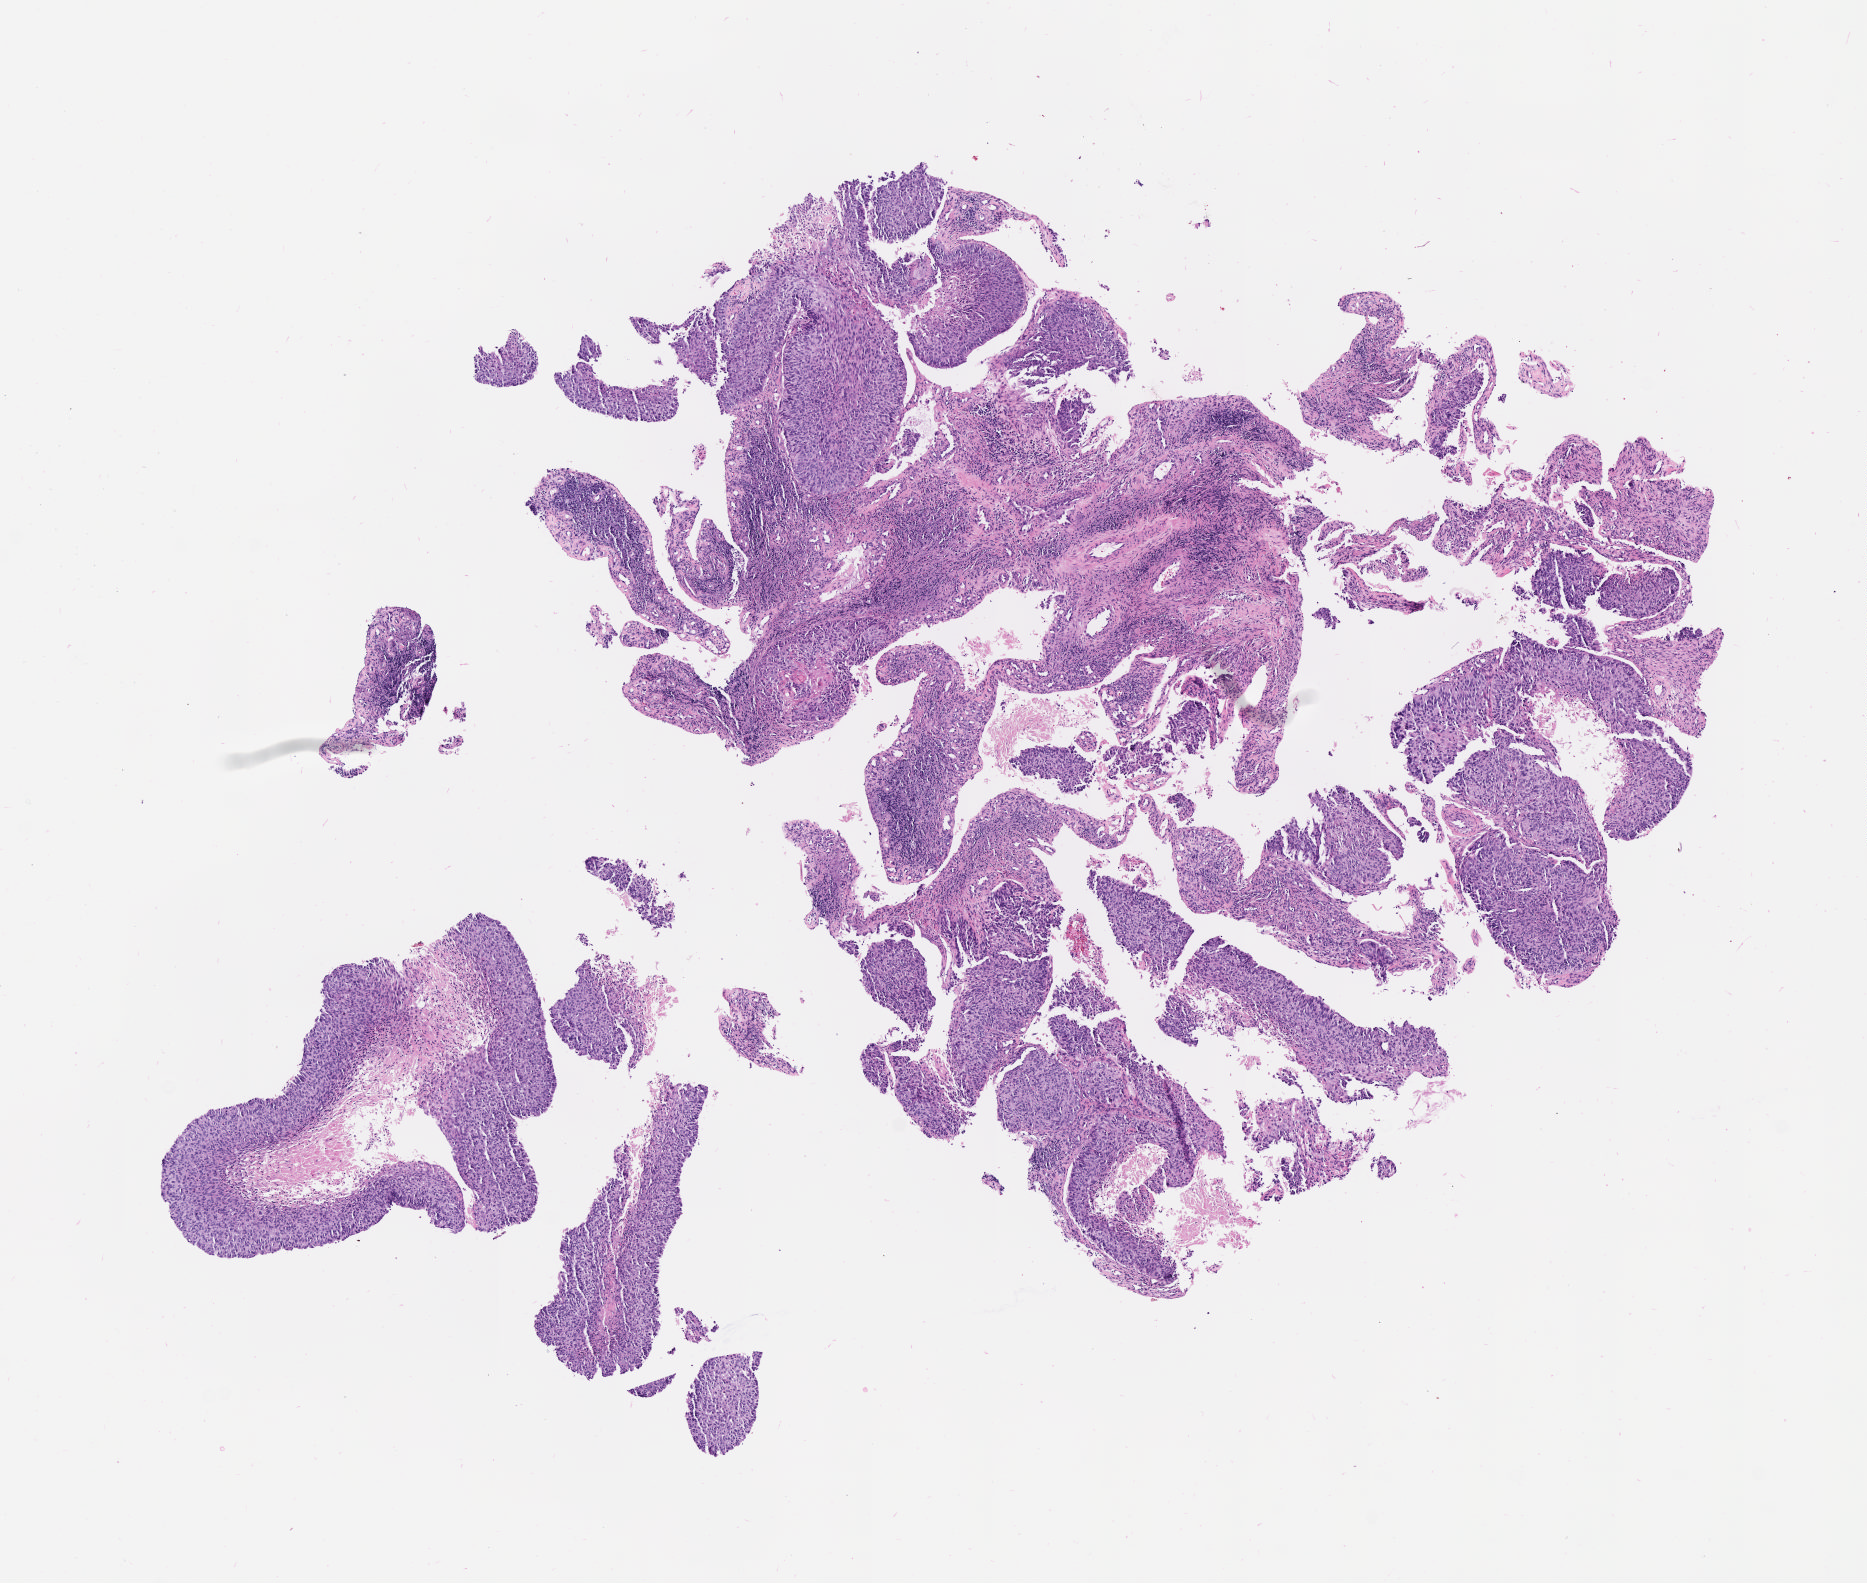
Digitized H&E-stained section, low-resolution overview of the scanned area, about 7.5 x 6.4 mm. Specimen: tumor tissue. Anatomic site: cervix. Patient: female, aged 48.
Histologic diagnosis: Squamous cell carcinoma, keratinizing, NOS.